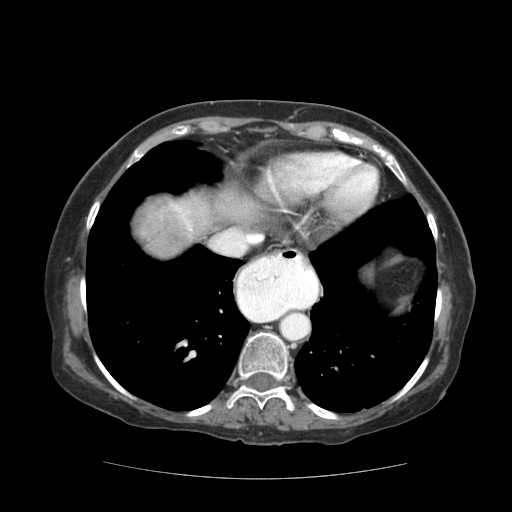
Contrast-enhanced abdominal CT (liver protocol), one axial slice; slice 97 of 111 in the series (ordered by position); reconstruction kernel STANDARD; 140 kVp; soft-tissue window (W 400 / L 40 HU); 2.5 mm slice thickness; 512 × 512 image matrix. Case-level facts recorded for this patient, not image findings: diagnosis: hepatocellular carcinoma (patient treated with transarterial chemoembolisation; whether this scan precedes or follows treatment is not stated here); TNM stage (as recorded): Stage-I; Child-Pugh class: A; tumour differentiation: moderately-poorly differentiated; tumour nodularity: uninodular.
Structures marked on this image (semi-automatic segmentation, software-assisted and operator-edited):
- abdominal aorta: bounding box <281,312,308,339> (left, top, right, bottom; pixels)
- liver parenchyma outside the tumour (the mass and vessels are separate outlines, so this box may not span the whole liver): <138,190,260,256>
- mass: <143,209,185,252>
- liver vessels: <177,207,191,230>